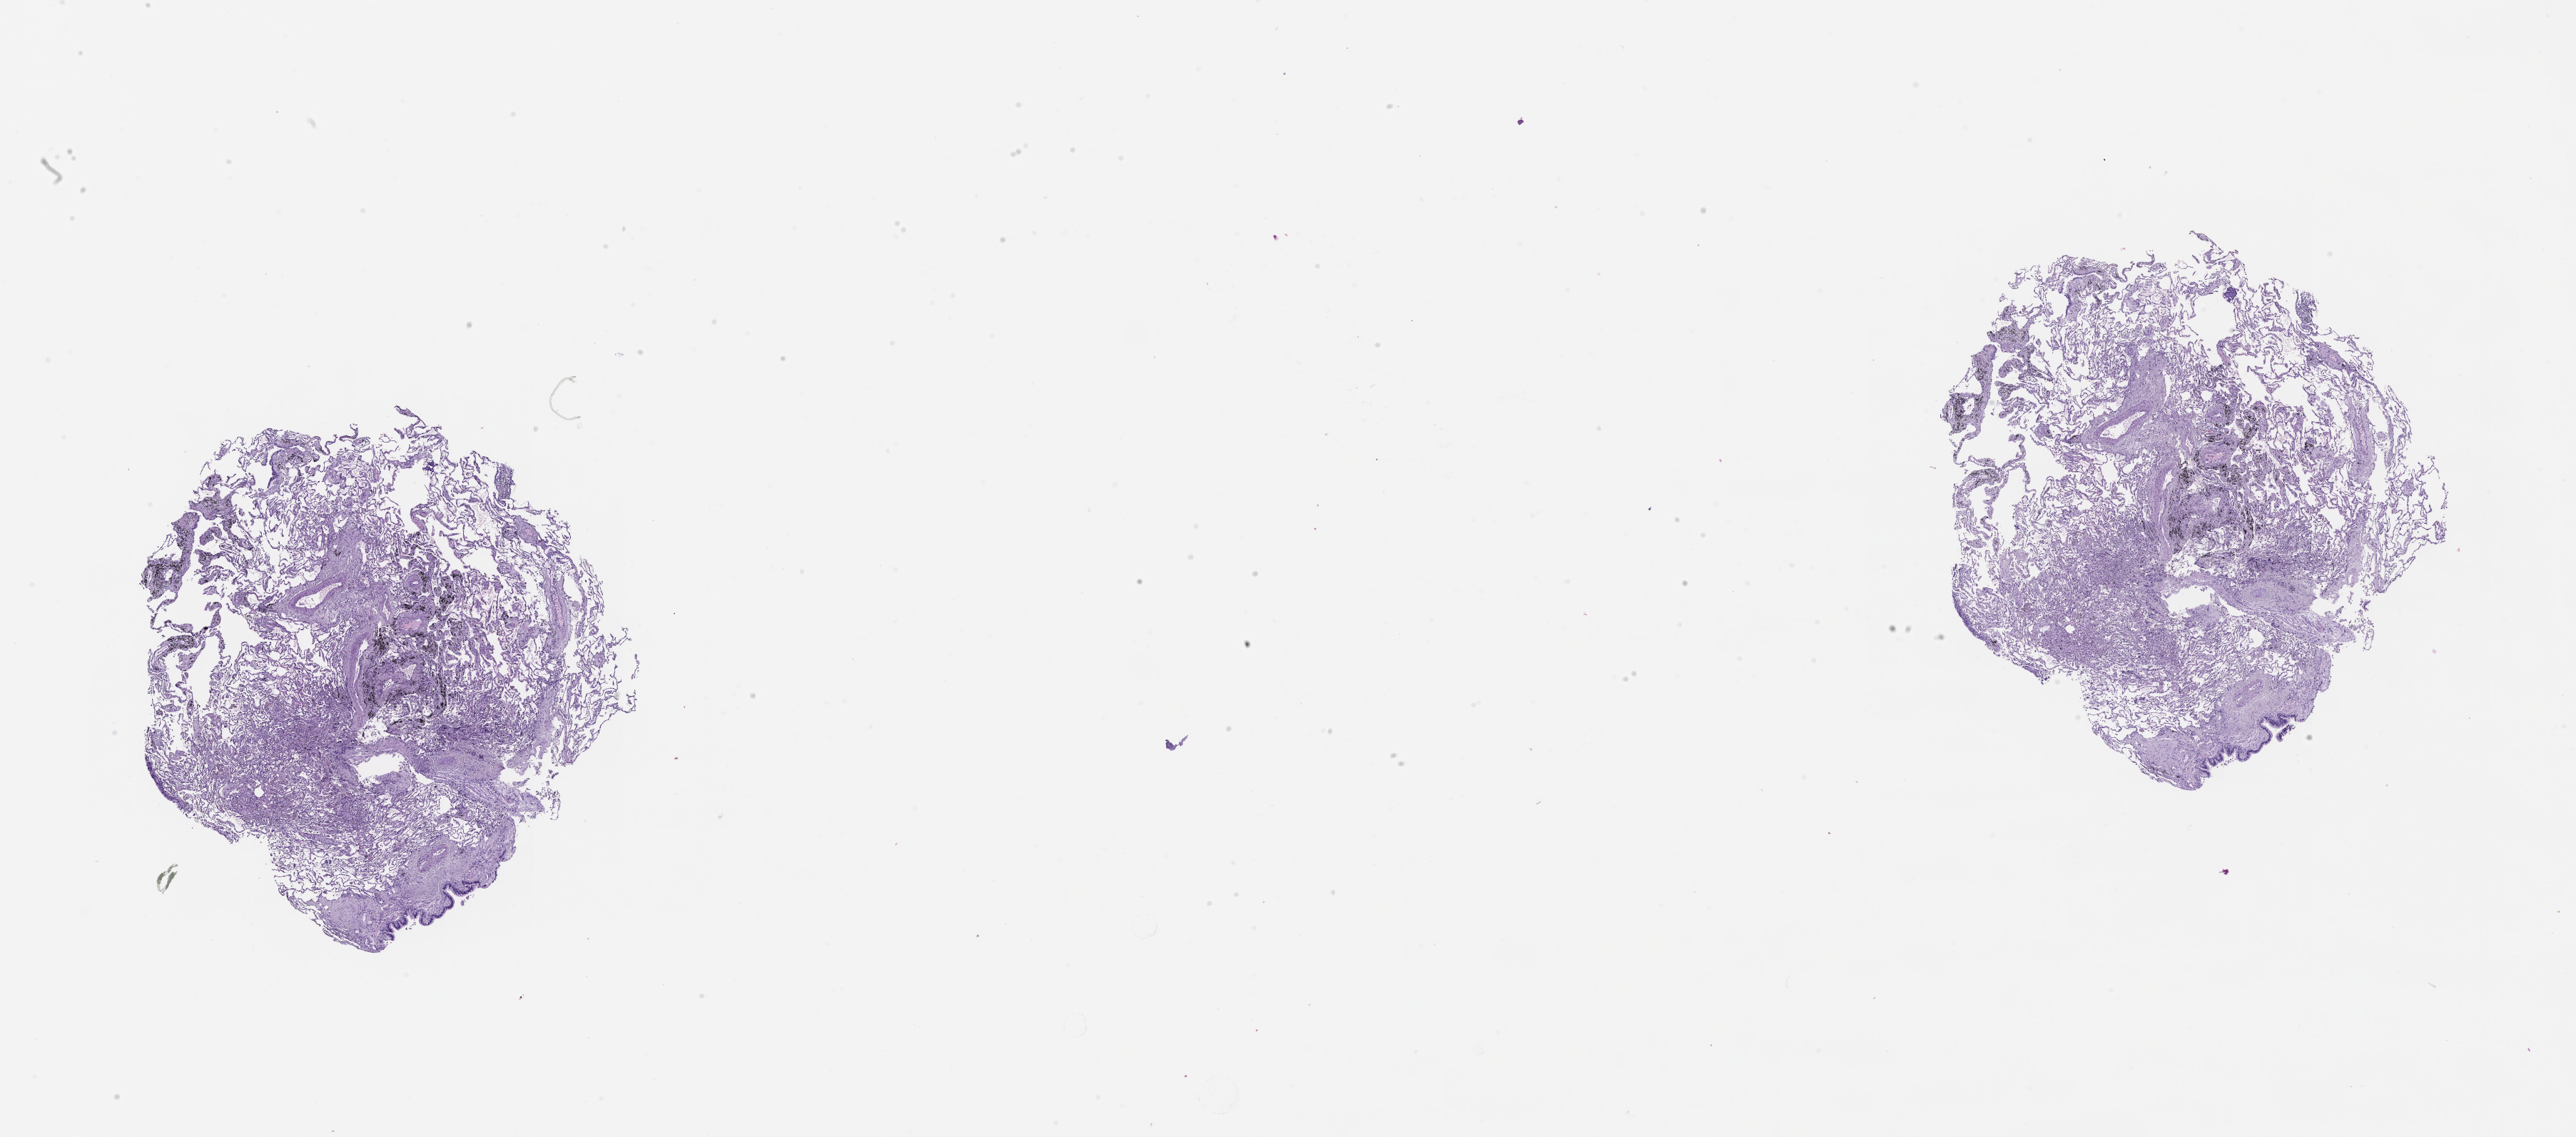
Whole-slide histology image, H&E, low-resolution overview of the scanned area, about 29.1 x 12.8 mm; lung, normal (non-tumour) tissue. Patient: male, age 63 years.
This section: normal (non-tumour) tissue from the same patient. Patient diagnosis (cohort enrolment): squamous cell carcinoma (lung).